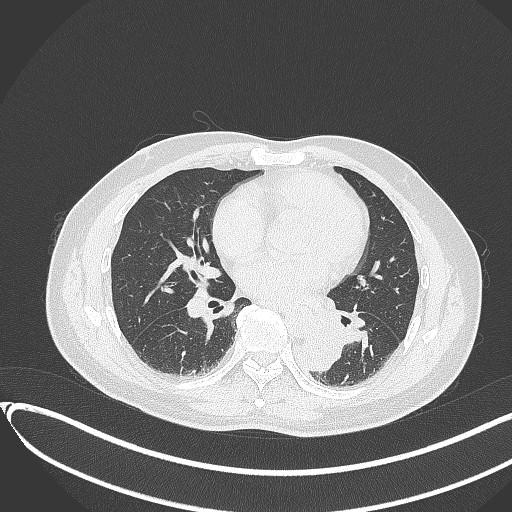
Chest CT, one axial slice; slice 153 of 417 in the series (ordered by position); reconstruction kernel B70f; 120 kVp; lung window (W 1500 / L -600 HU); 1 mm slice thickness; 512 × 512 image matrix. Patient: male, 54 years. From the clinical record (not read from this slice): clinical TNM (as recorded): T3 N0 M0.
Outlined on this slice (rectangle marked by the reading radiologist):
- lung tumour (recorded histology: squamous cell carcinoma): bounding box [x1, y1, x2, y2] px = [301, 324, 344, 378]